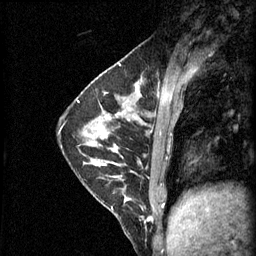
Breast MRI (dynamic contrast-enhanced), one sagittal slice. Position 18 of 60 along the scan axis. 3 images stored at this slice position (order not interpretable as contrast timing). 1.5 T. TE 4.2 ms, TR 11 ms. 2.1 mm slice thickness. 256 × 256 image matrix, field of view 180 × 180 mm. Patient: female, 29 years.
Annotated regions visible in this slice (semi-automatically segmented with operator editing):
- analysis volume of interest (the breast-tissue region the enhancement analysis was run in; not a lesion): box from (x=93, y=164) to (x=153, y=225) px
- tumour enhancement mask (voxels above the 70 % enhancement threshold inside the analysis volume of interest): (x=93, y=164)–(x=152, y=221)